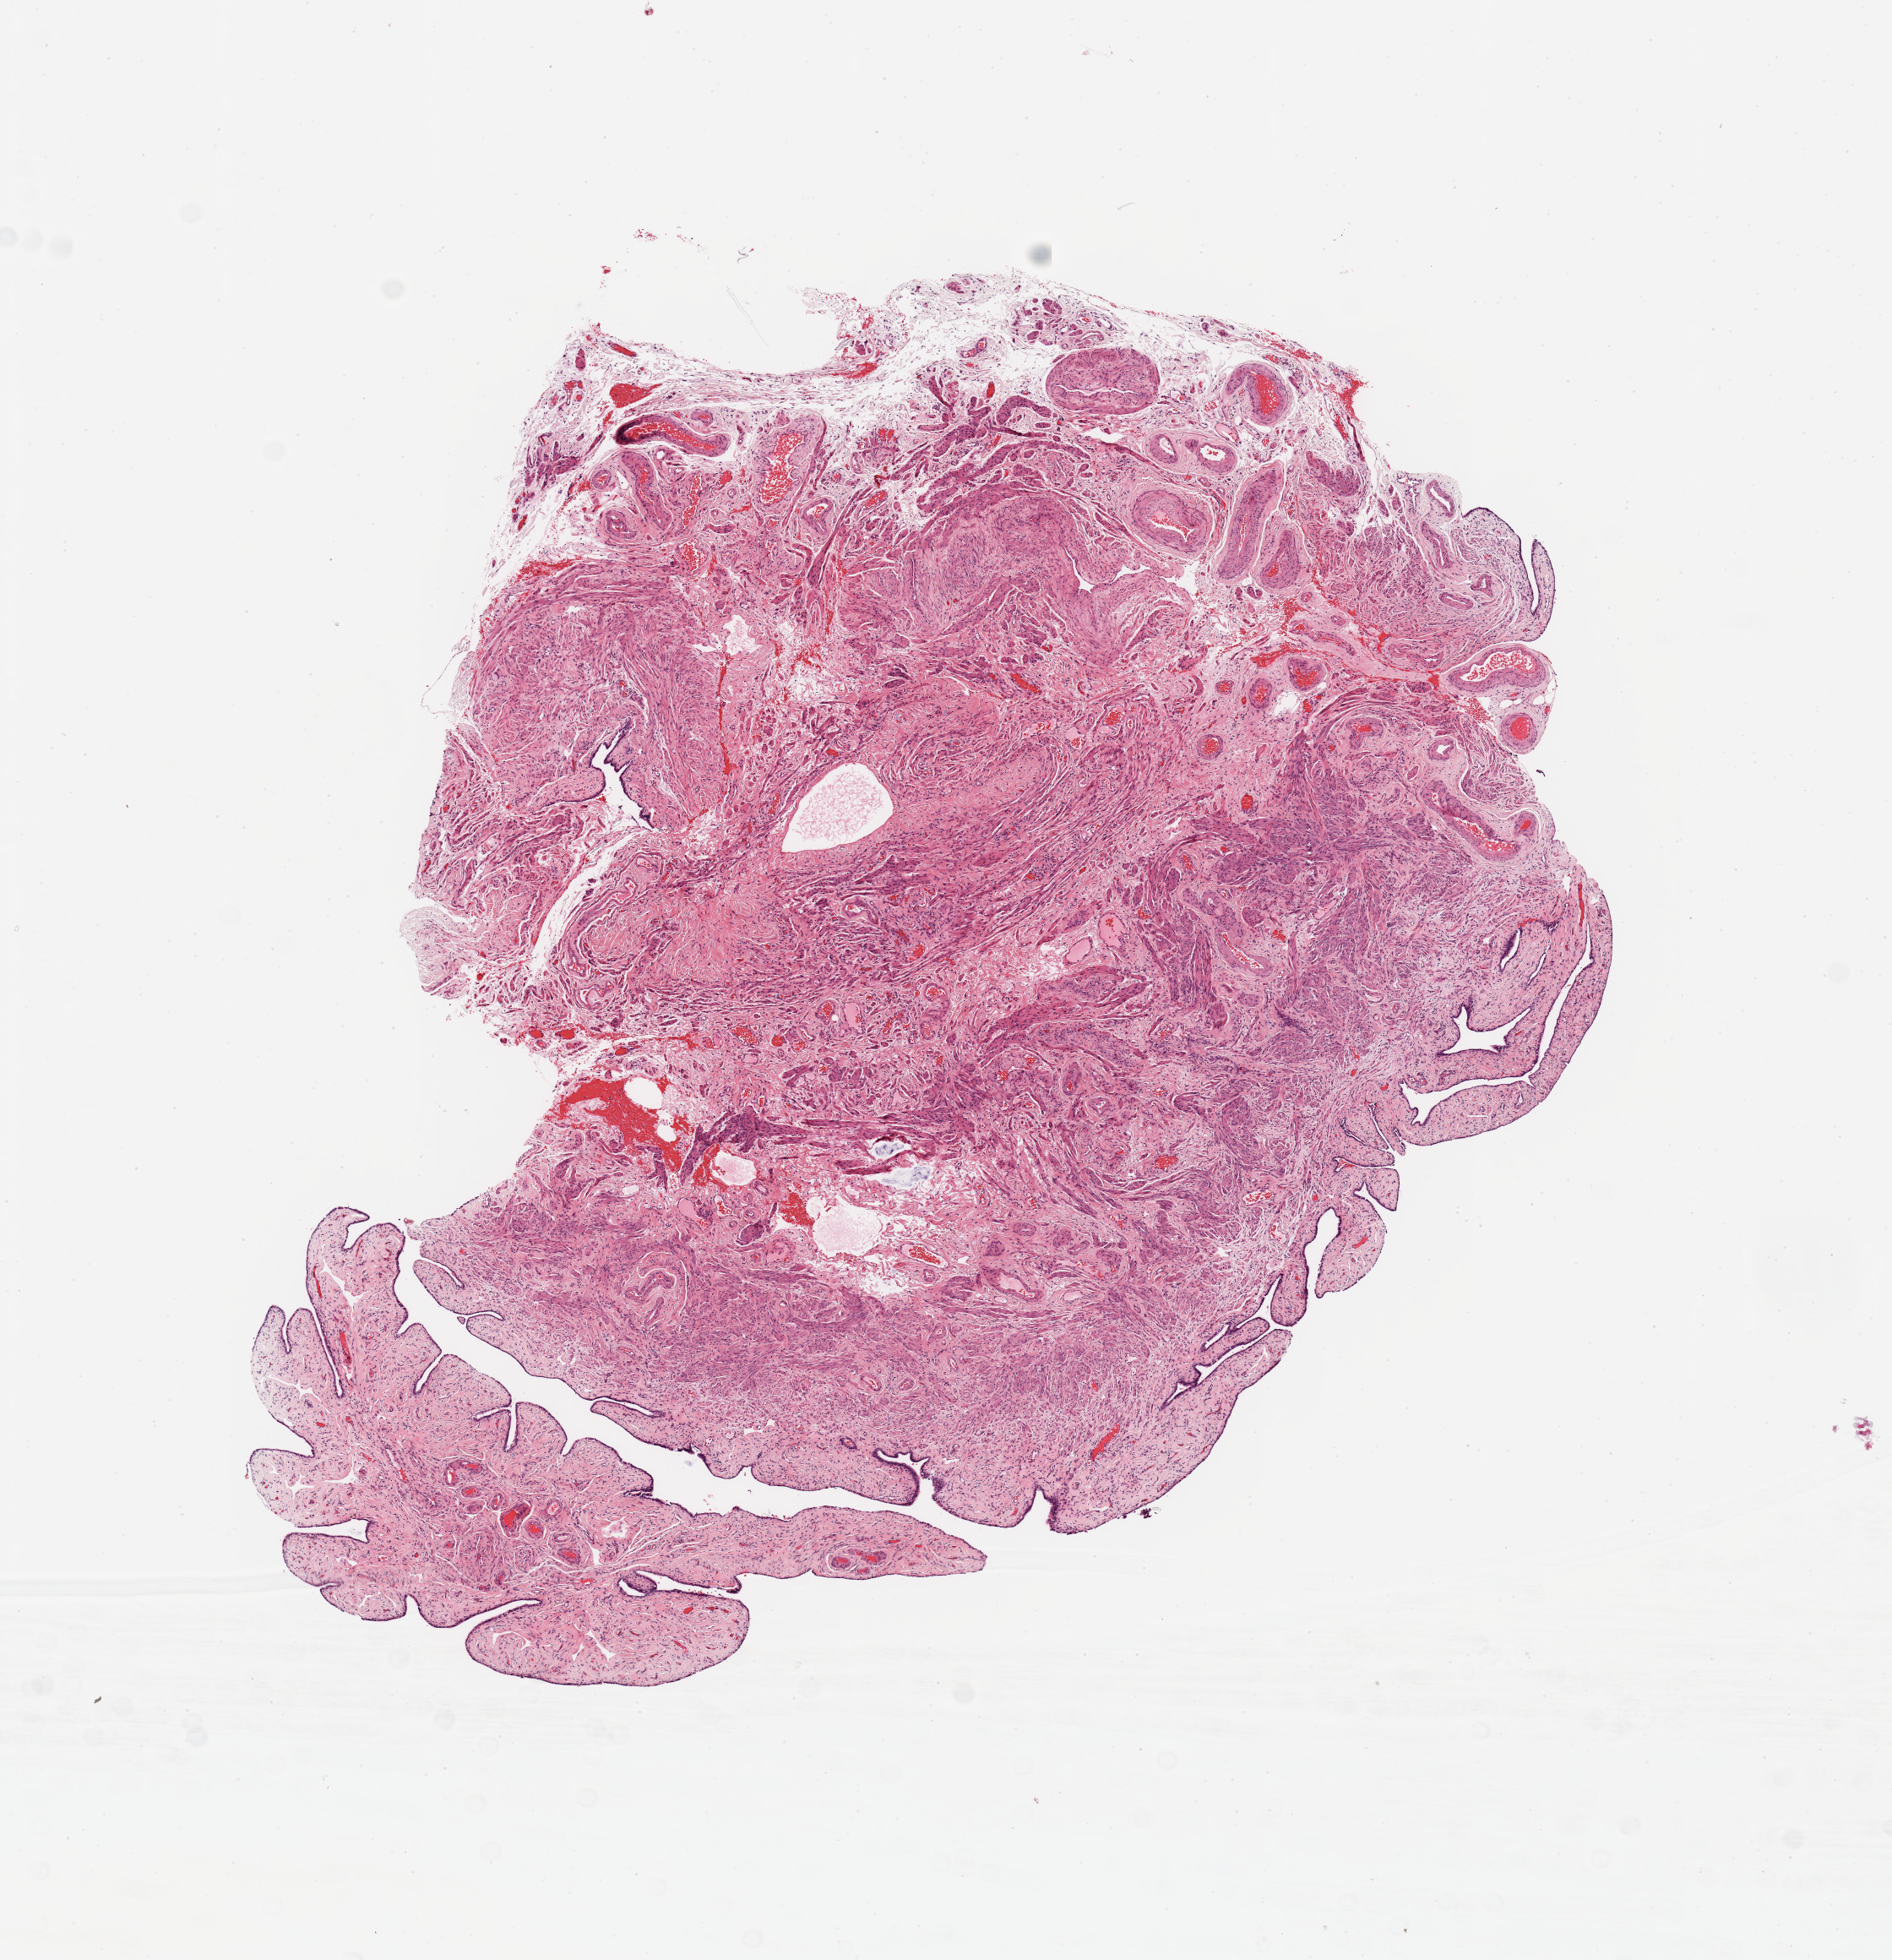
Hematoxylin and eosin (H&E) stained whole-slide image — whole scanned area (about 8.9 x 9.2 mm, slide scanned at 20x) shown as a low-resolution overview; normal (non-tumour) tissue sample, uterus. Patient: female, age 73 years.
* this section: normal (non-tumour) tissue from the same patient
* patient diagnosis: Endometrioid adenocarcinoma, NOS